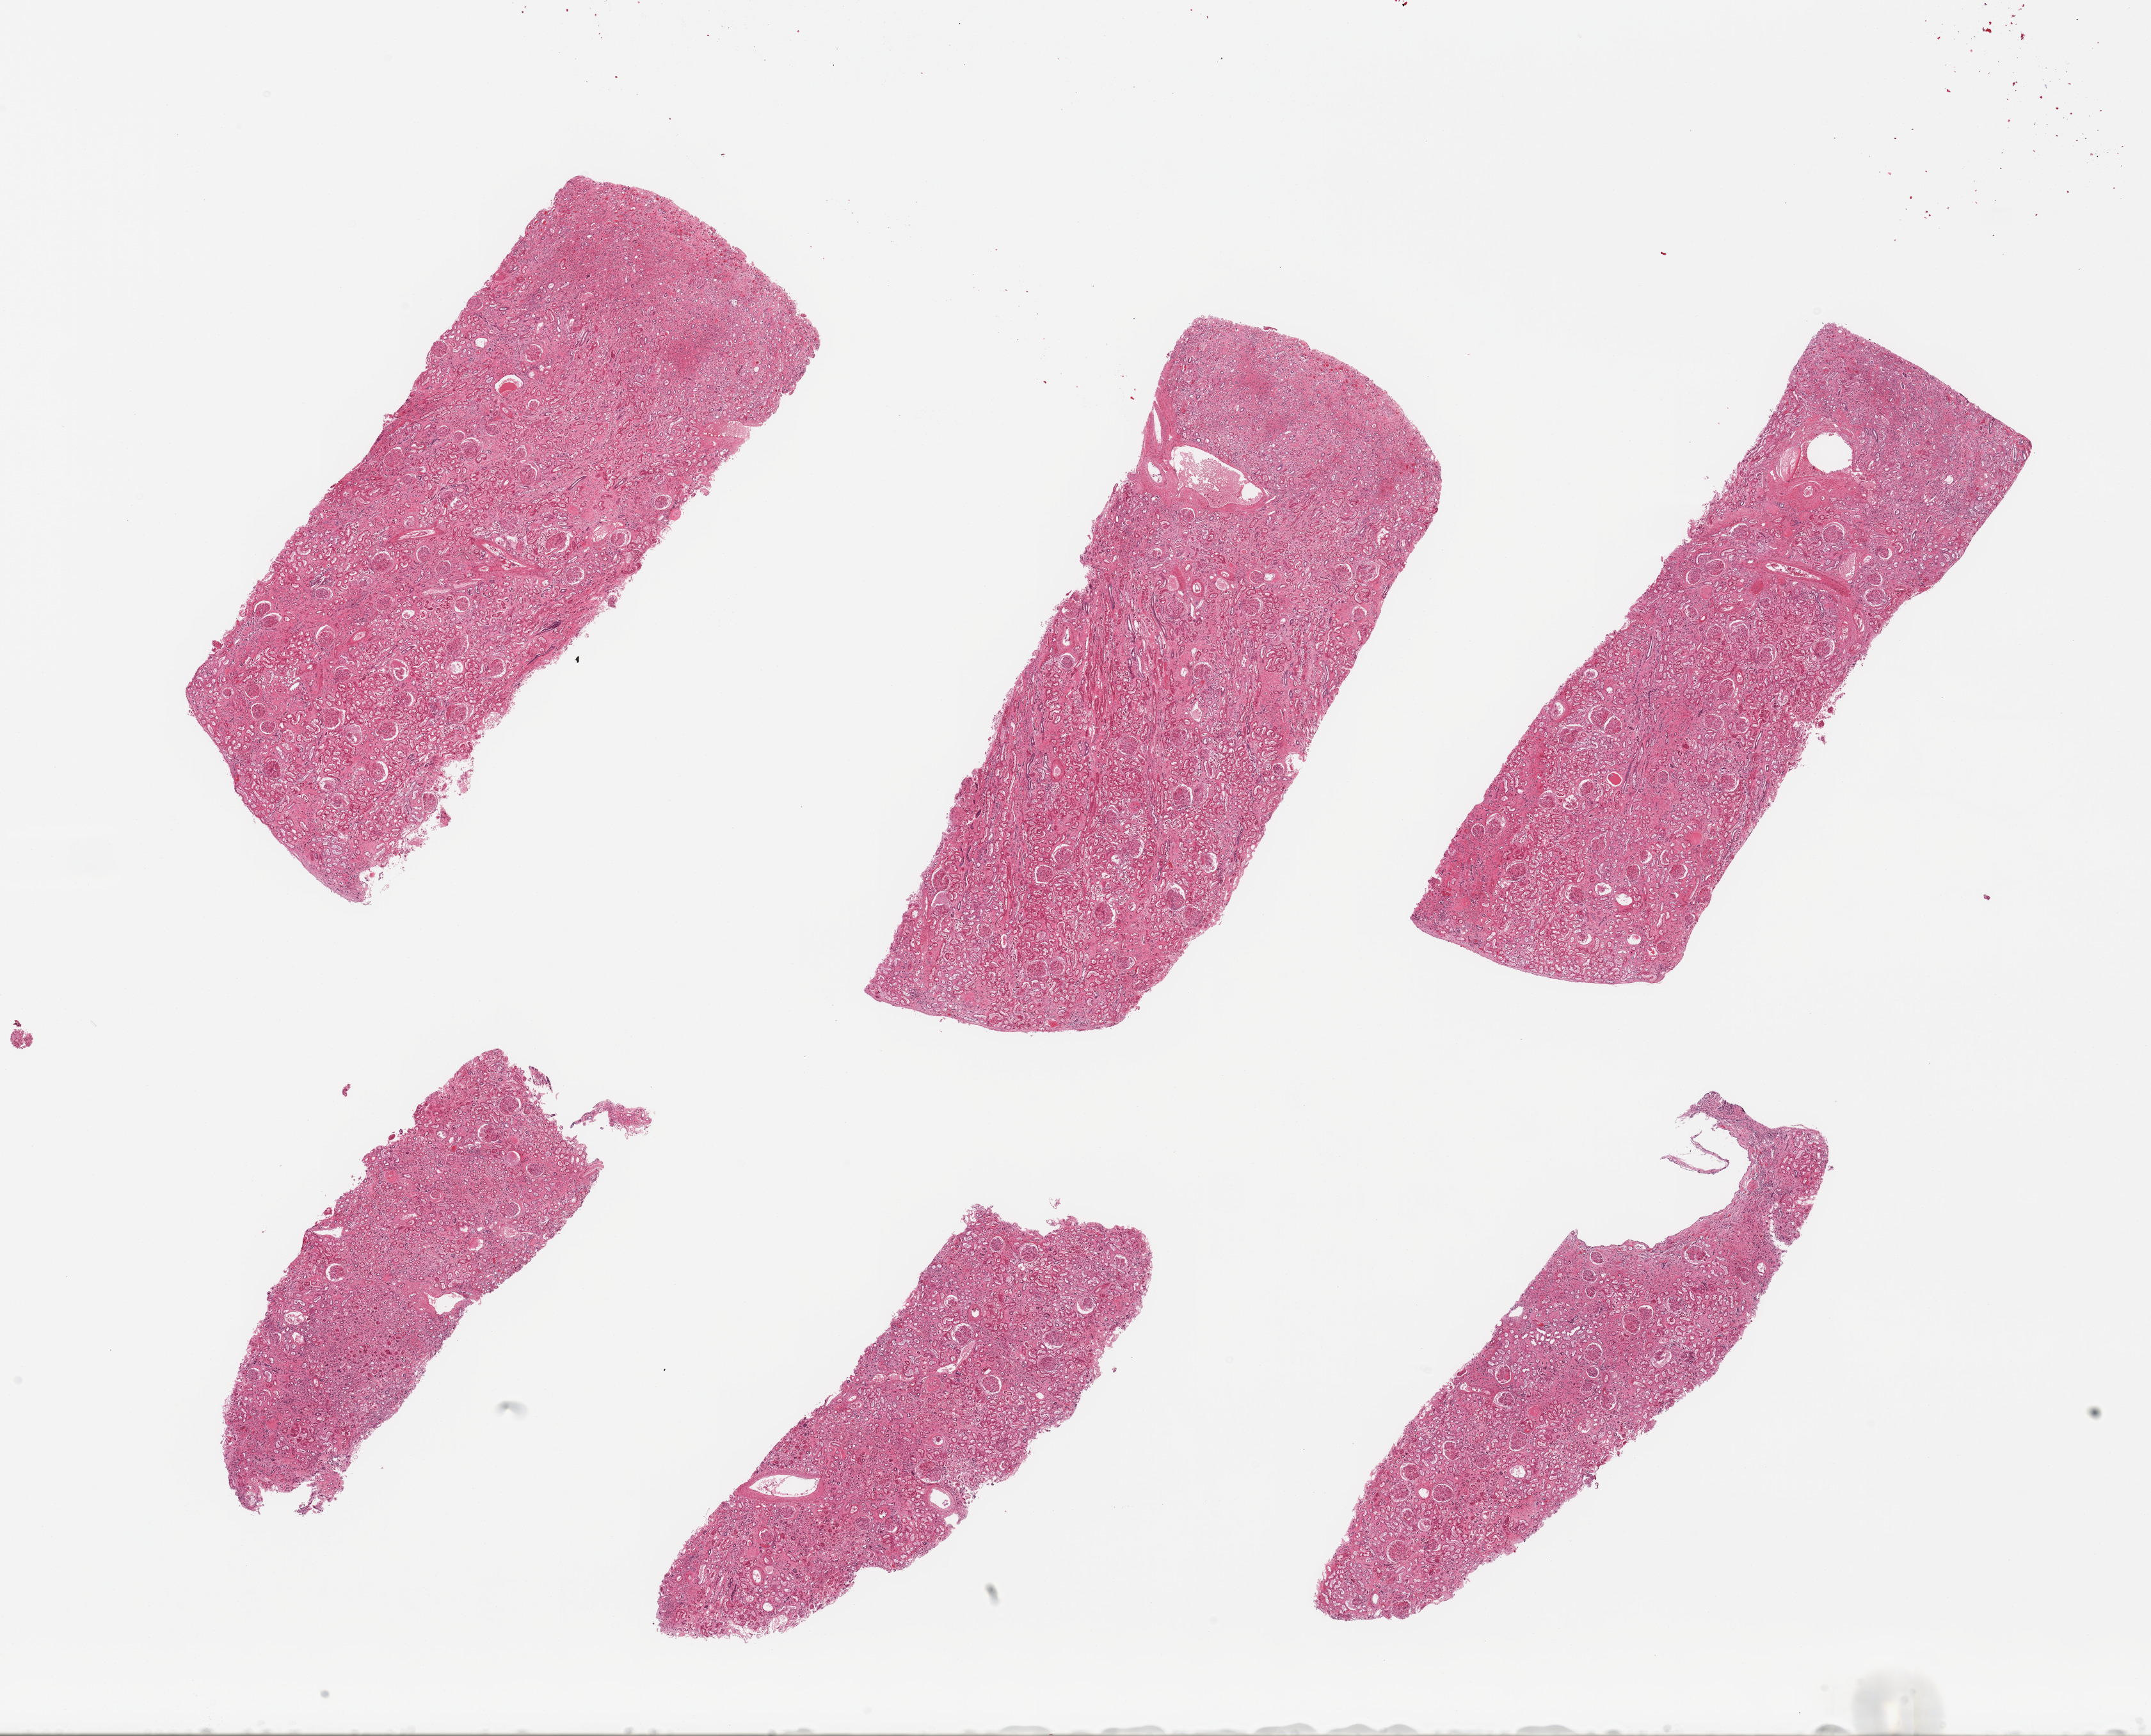
Digitized hematoxylin and eosin (H&E)-stained section, brightfield, a low-resolution overview of the entire scanned area, about 26.6 x 21.5 mm; PAXgene-fixed, paraffin-embedded tissue; target tissue: renal cortex; donor tissue sample. Donor sex: male.
• reviewer comment on this tissue sample: 6 pieces, glomeruli present with mesangial hyalin deposits; advanced tubular autolysis, interstitial fibrosis